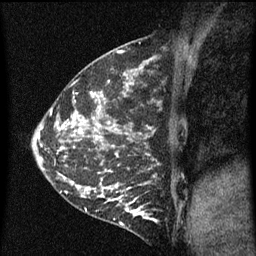
Breast MRI (dynamic contrast-enhanced), one sagittal slice; position 18 of 60 along the scan axis; dynamic contrast-enhanced series, image 2 of 5 at this slice position (ordered by acquisition); 1.5 T; TE 4.2 ms, TR 8 ms; 2 mm slice thickness; 256 × 256 image matrix. Patient: female, 35 years.
Structures marked on this image (semi-automatic segmentation, software-assisted and operator-edited):
- analysis volume of interest (the breast-tissue region the enhancement analysis was run in; not a lesion): bounding box <118,196,158,229> (left, top, right, bottom; pixels)
- tumour enhancement mask (voxels above the 70 % enhancement threshold inside the analysis volume of interest): <120,196,158,223>